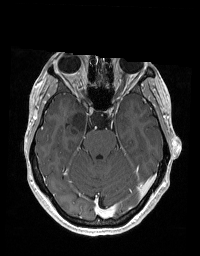
Brain MRI from a brain-tumour surgery series, one axial slice. Slice 123 of 192 in the series (ordered by position). T1-weighted post-contrast. 200 × 256 image matrix. From the clinical record (not read from this slice): histopathology: Glioblastoma; WHO grade: 2; IDH mutation: no.
Structures marked on this image (manually delineated by an expert):
- tumour: box from (x=72, y=112) to (x=101, y=134) px